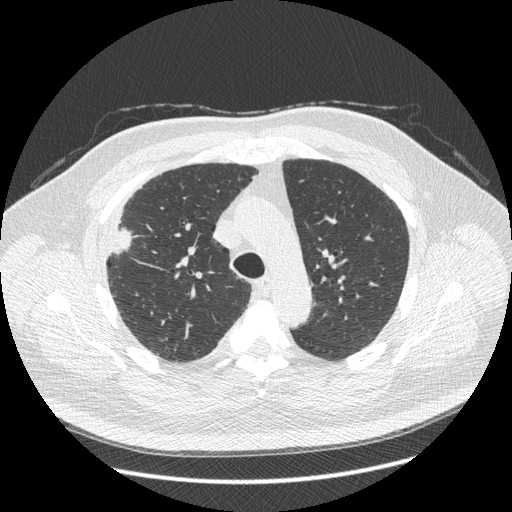
Low-dose screening chest CT, one axial slice. Slice 310 of 426 in the series (ordered by position). 120 kVp. Lung window (W 1500 / L -600 HU). 1.25 mm slice thickness. 512 × 512 image matrix, field of view 400 × 400 mm.
Structures marked on this image (expert manual segmentation):
- lesion 1 (tumor, upper lobe of right lung): box from (x=113, y=229) to (x=132, y=253) px